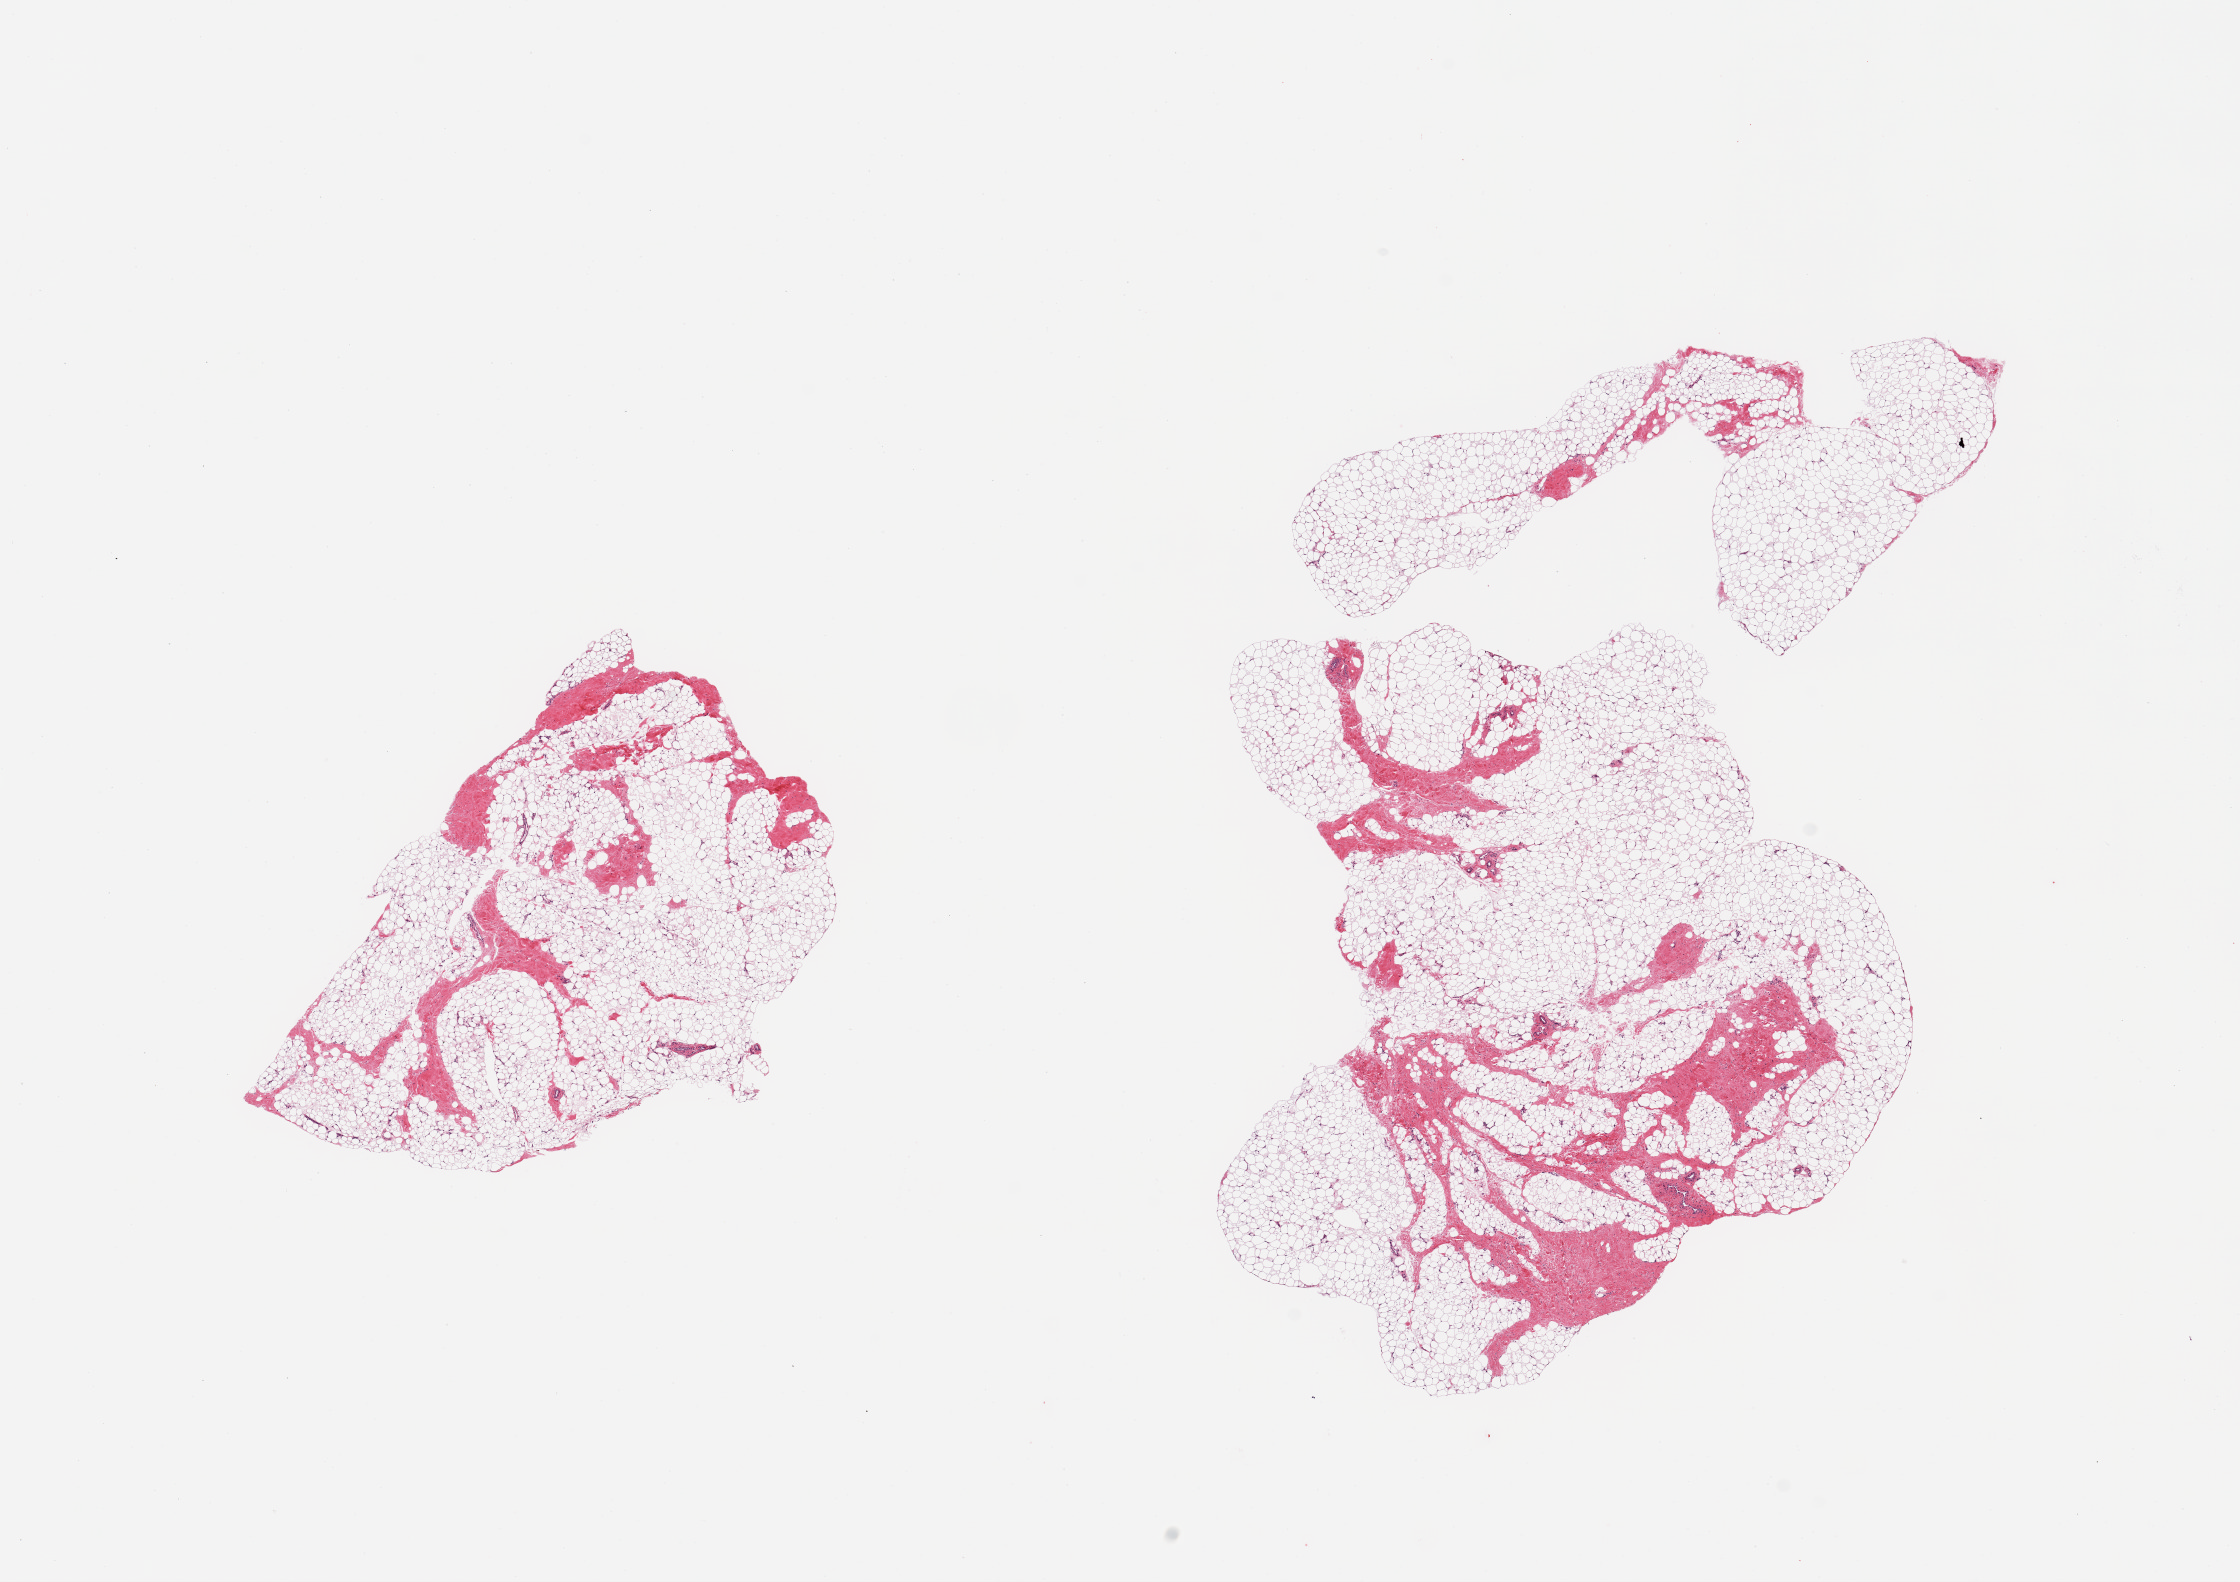
Digitized haematoxylin and eosin-stained section, whole scanned area (about 17.7 x 12.5 mm) shown as a low-resolution overview; PAXgene-fixed, paraffin-embedded tissue; section of breast (target tissue); donor tissue sample. Donor sex: male.
Pathologist's review note for this sample: 2 pieces, fibroadipose elements only.